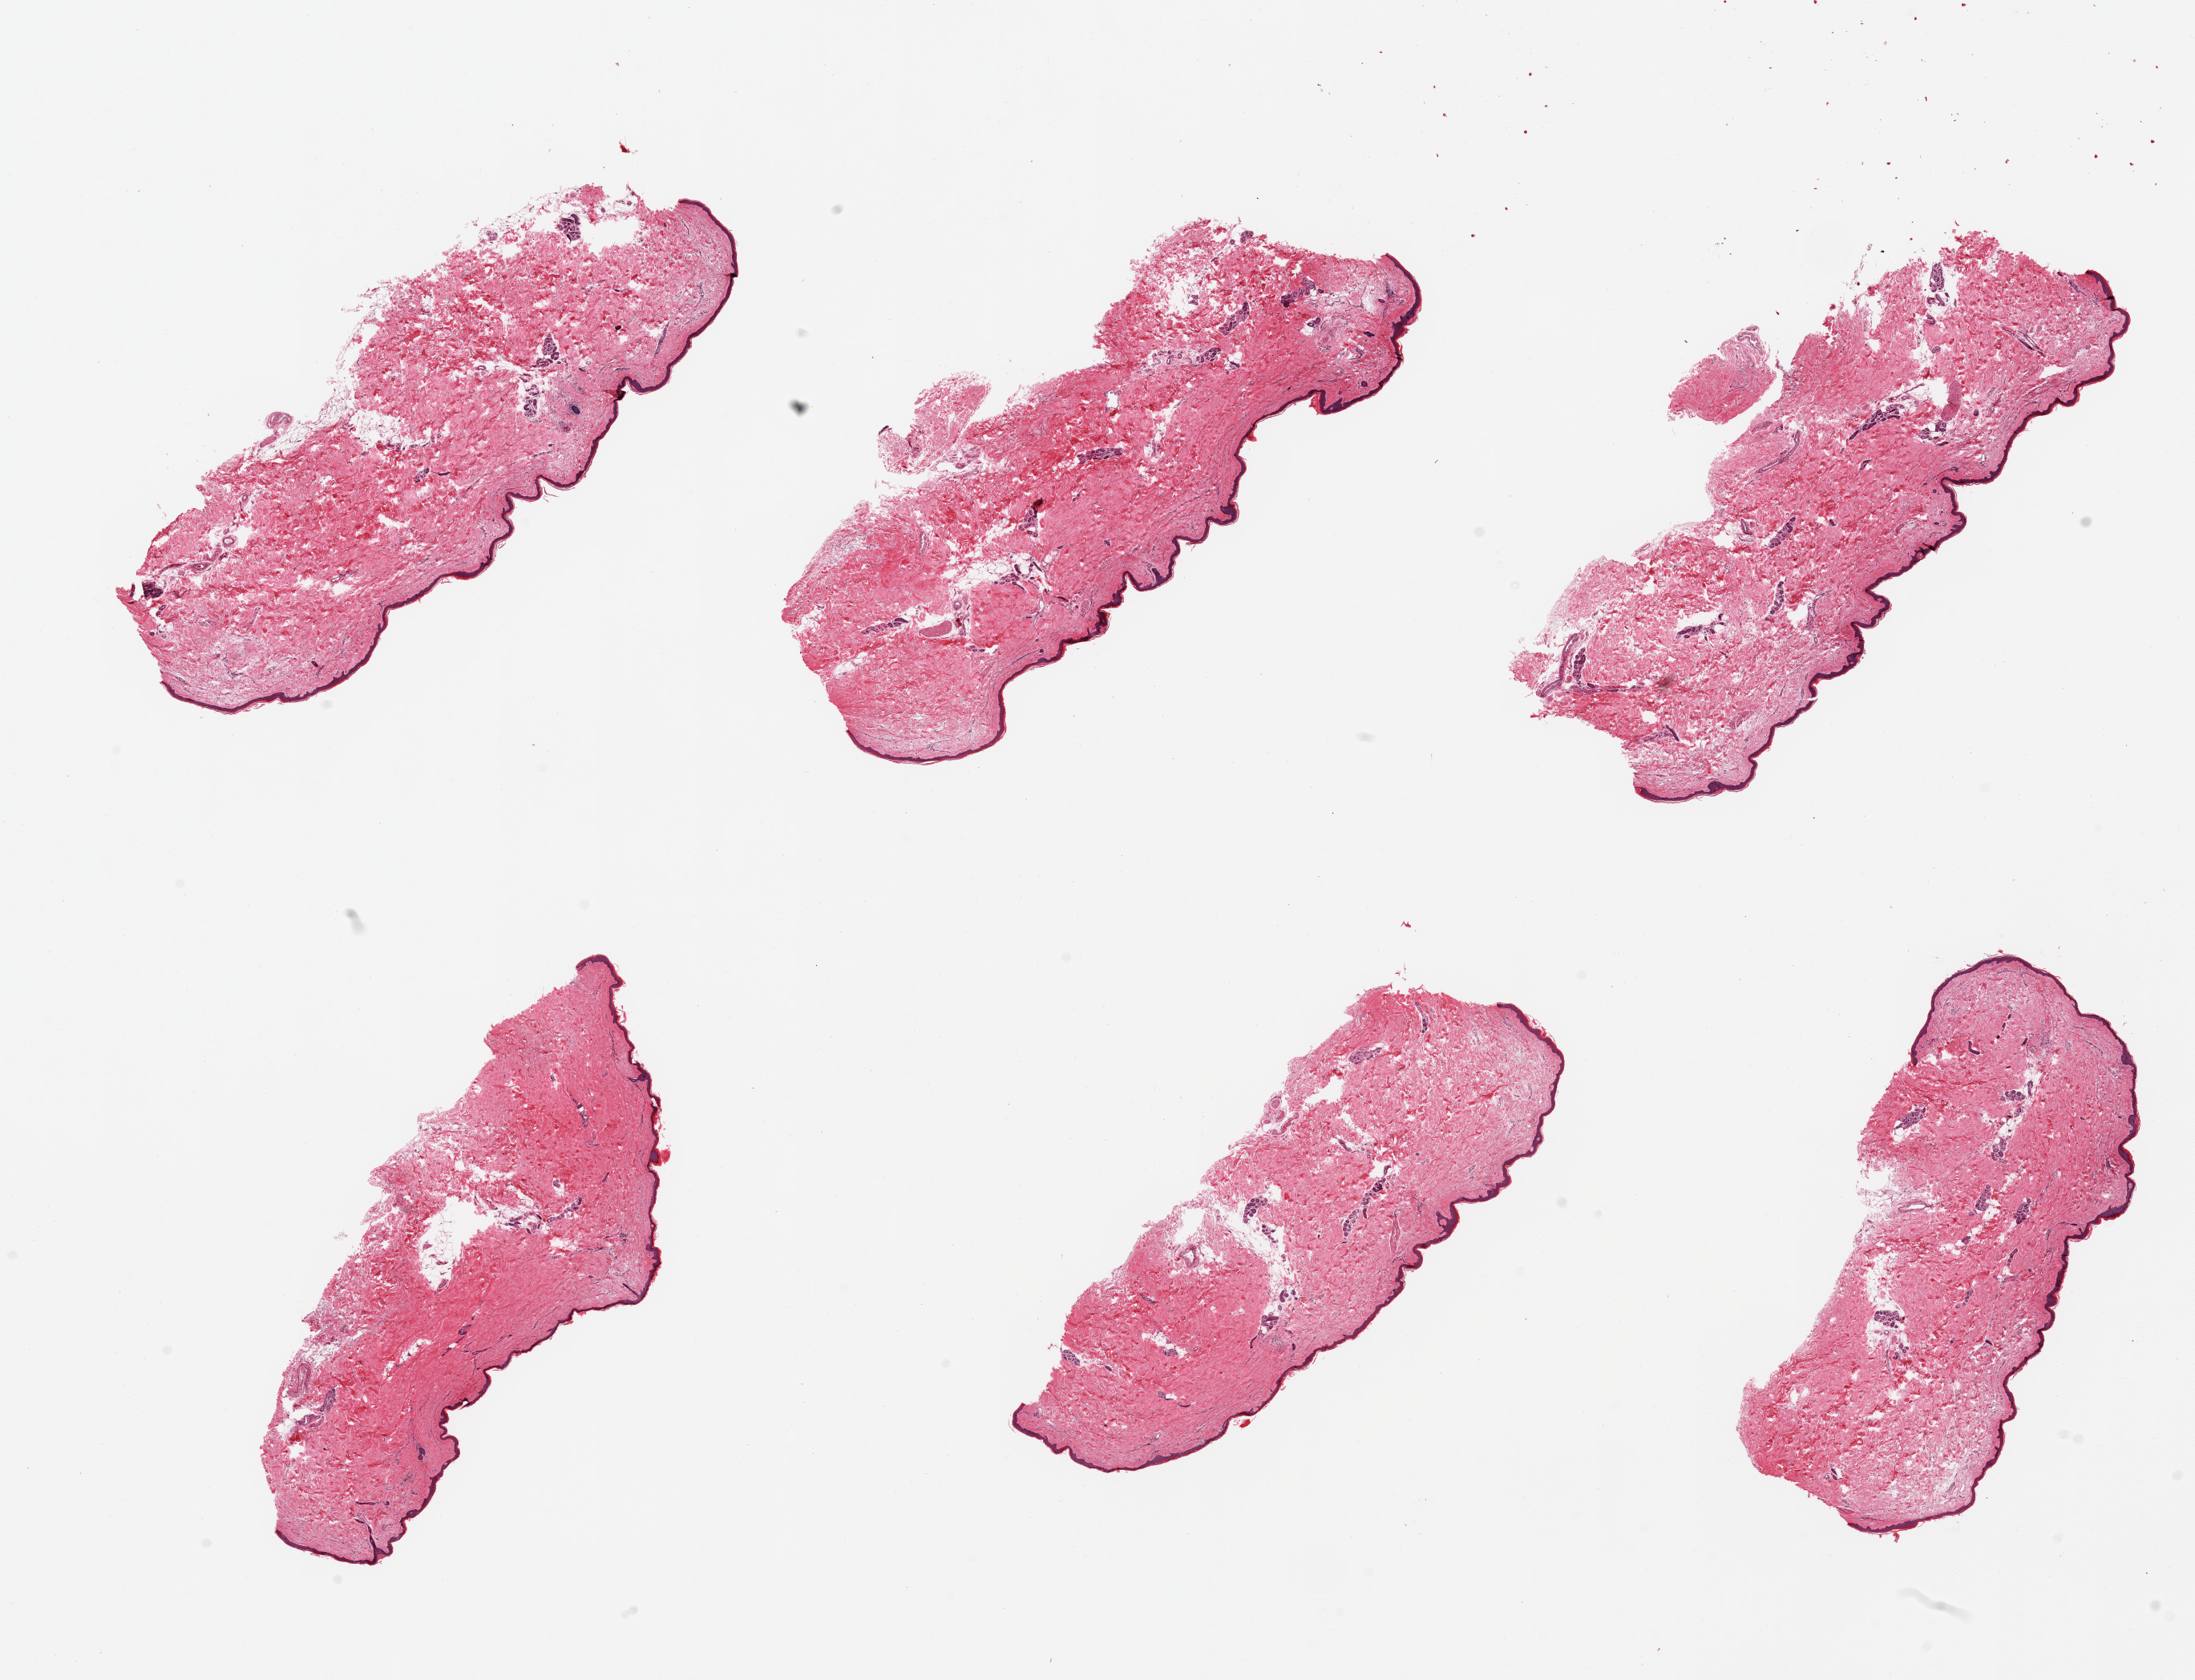
H&E whole-slide image, brightfield, whole scanned area (about 21.7 x 16.6 mm) shown as a low-resolution overview. PAXgene-fixed, paraffin-embedded tissue. Section of skin of lower leg (target tissue). Tissue donor sample. Donor sex: female.
• review note (as recorded): 6 pieces; well trimmed; 5% dermal fat